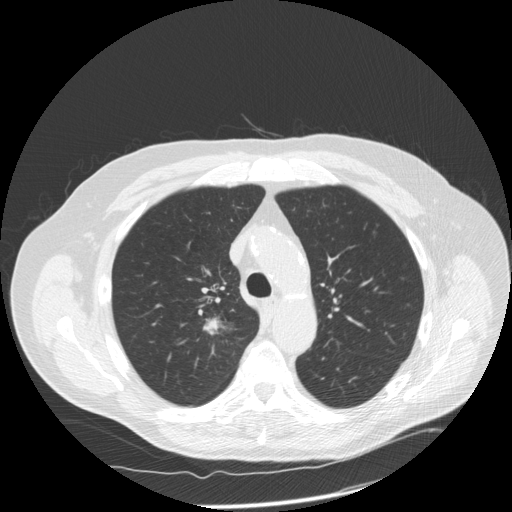
Low-dose screening chest CT, one axial slice. Reconstruction kernel STANDARD. Lung window (W 1500 / L -600 HU). 2.5 mm slice thickness. 512 × 512 image matrix, field of view 390 × 390 mm.
Structures marked on this image (outlined manually by an expert reader):
- lesion 1 (tumor, upper lobe of right lung): bounding box <205,319,218,332> (left, top, right, bottom; pixels)